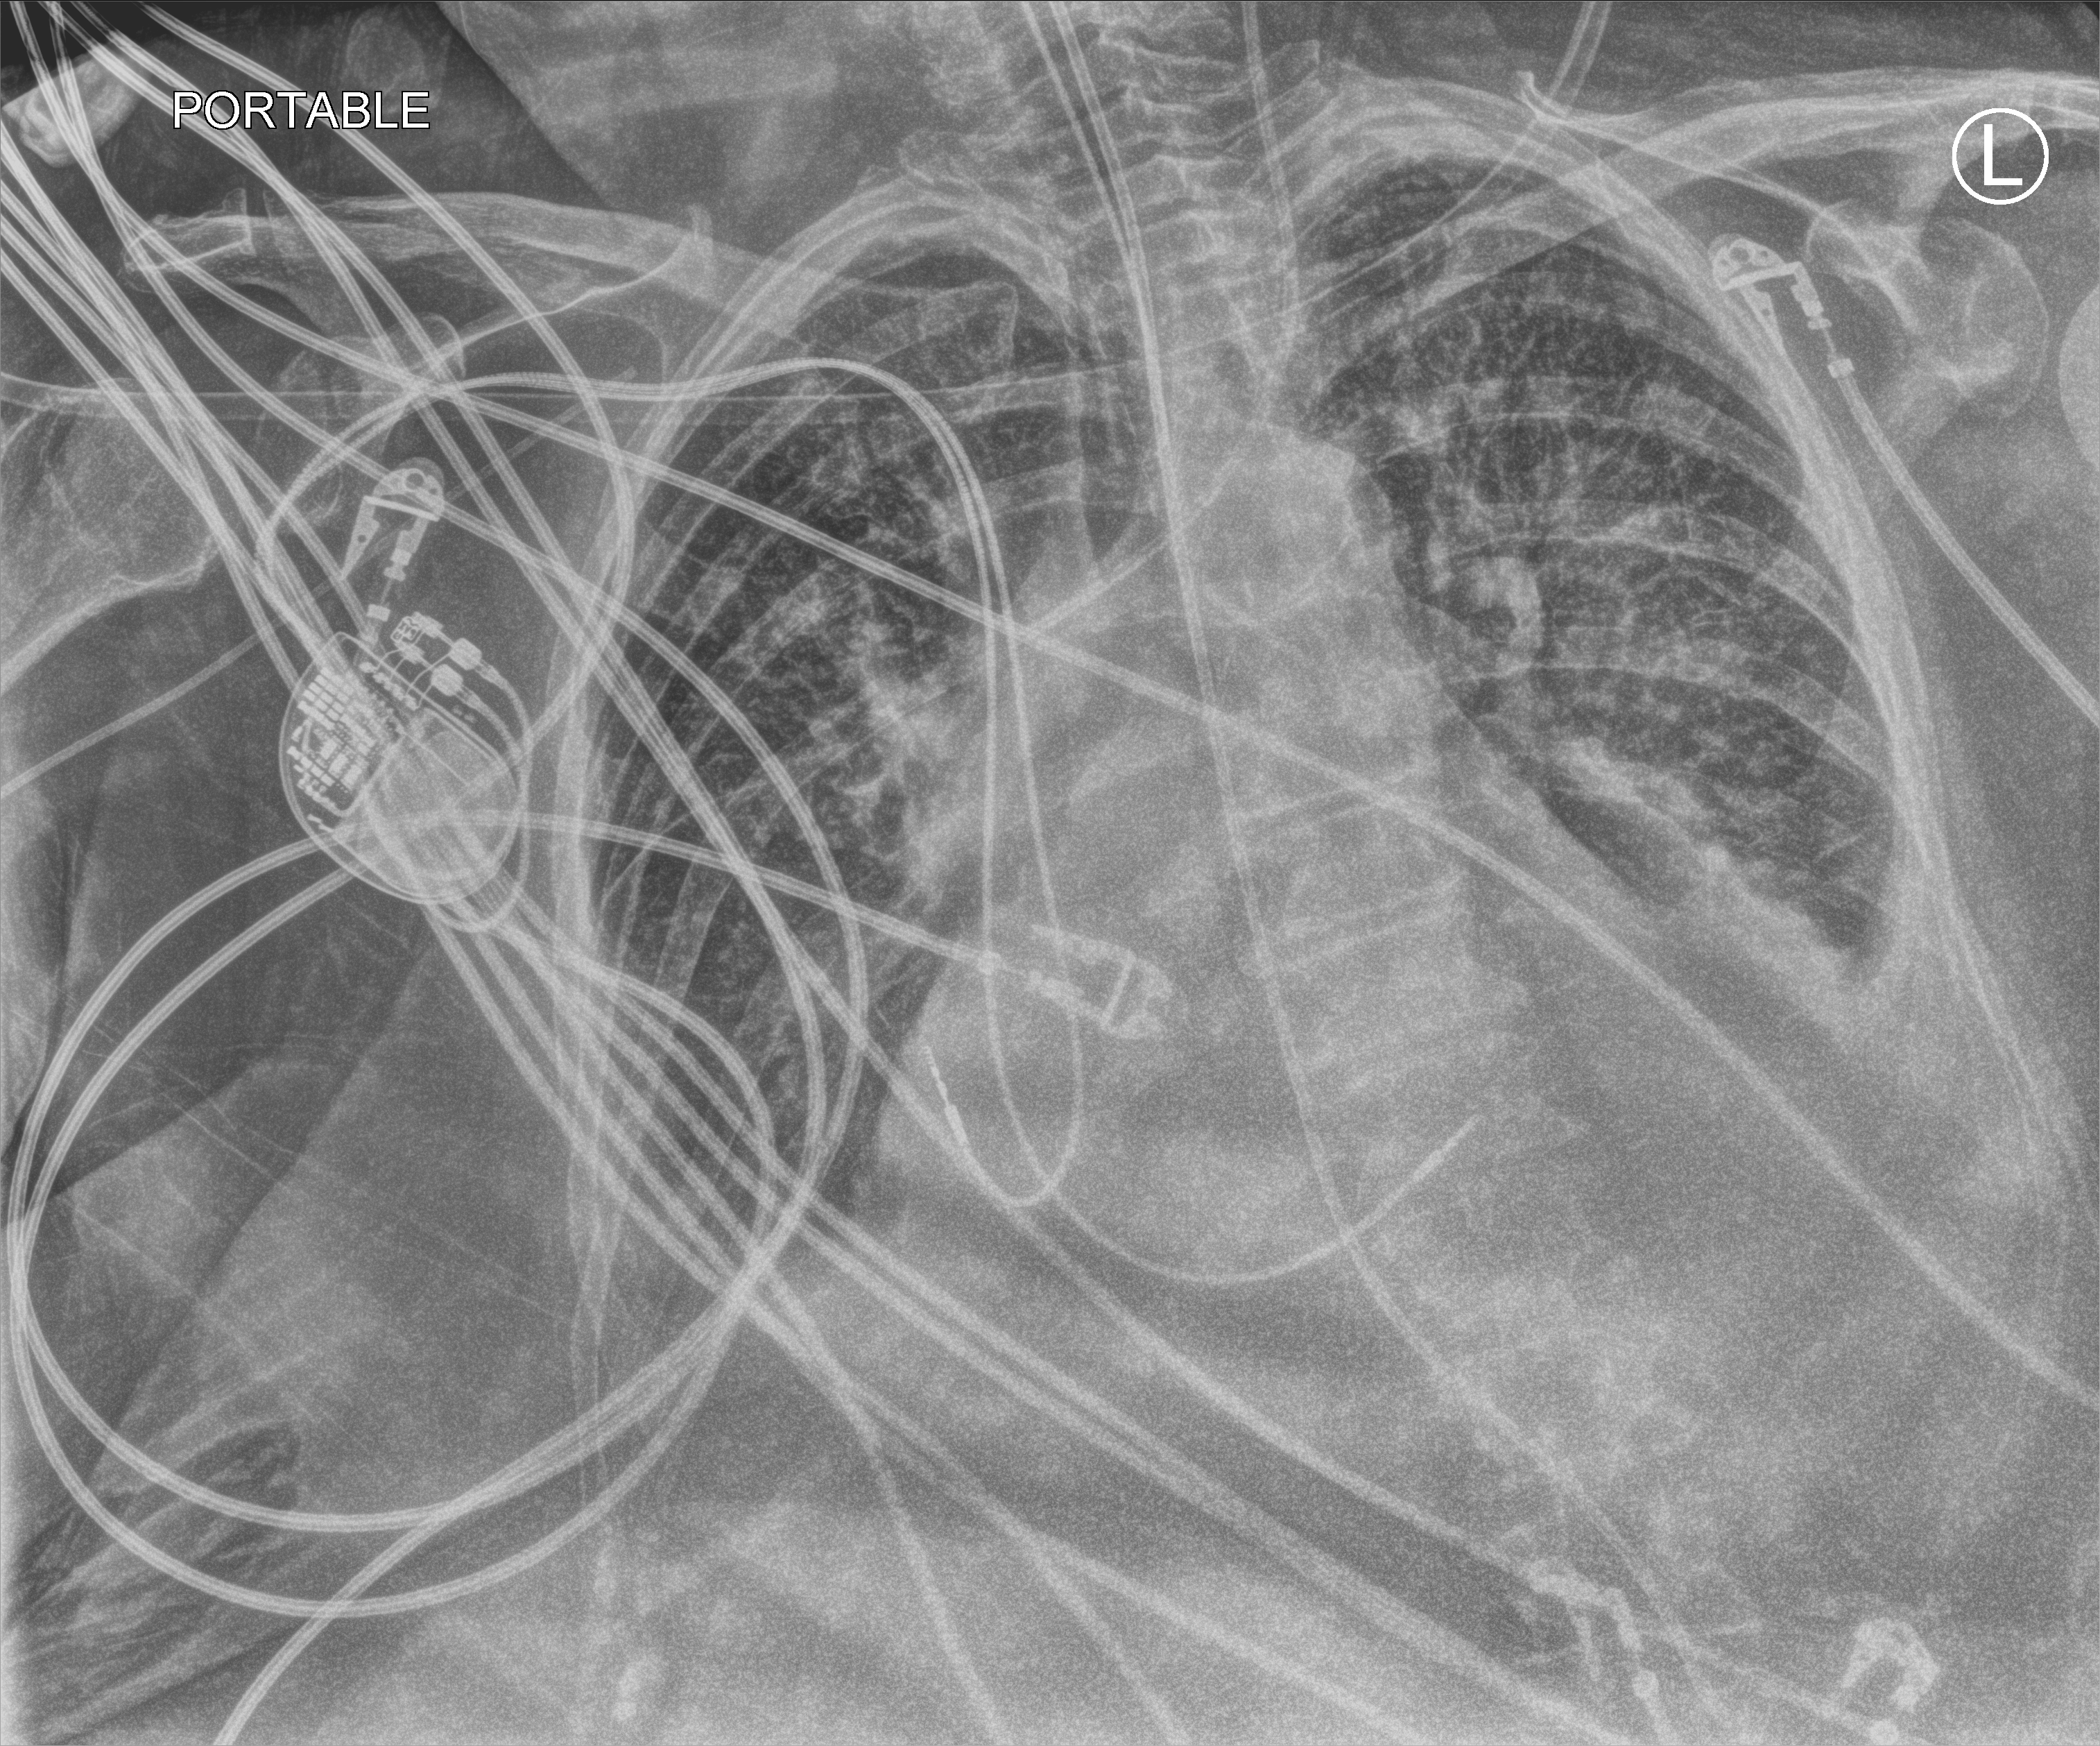
Chest X-ray (portable). Female patient hospitalised with COVID-19, age 75–90 years.
From the hospital-stay record, not from the radiograph (when in the stay this image was taken is not recorded):
- admitted to intensive care during this hospital stay: yes